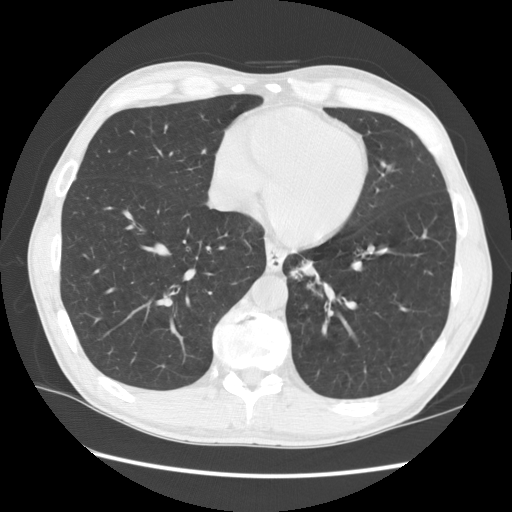
Low-dose screening chest CT, one axial slice. Slice 43 of 141 in the series (ordered by position). Lung window (W 1500 / L -600 HU). 2.5 mm slice thickness. 512 × 512 image matrix.
Outlined on this slice (manually delineated by an expert):
- lesion 2 (nodule, lower lobe of left lung): bounding box (x1, y1, x2, y2) in pixels: (300, 261, 316, 280)